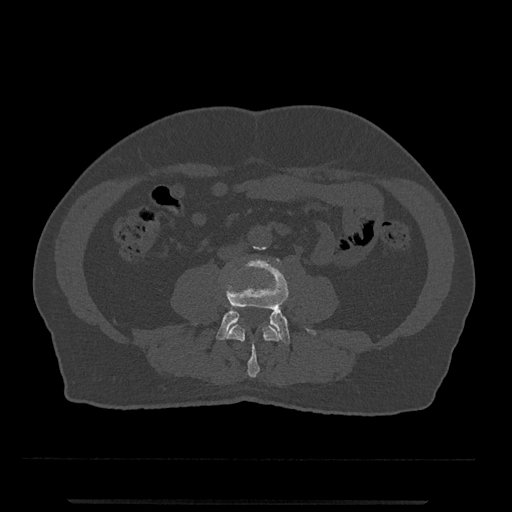
CT including the spine, one axial slice. Position 164 of 797 along the scan axis. Reconstruction kernel Br40s/3. Bone window (W 1800 / L 400 HU). 0.5 mm slice thickness. 512 × 512 image matrix, field of view 419 × 419 mm. Male patient, age 63 years. Case-level facts recorded for this patient, not image findings: primary cancer: prostate.
Outlined on this slice (semi-automatically segmented with operator editing):
- L3 vertebra: bounding box (x1, y1, x2, y2) in pixels: (226, 324, 280, 378)
- L4 vertebra: (216, 259, 316, 344)